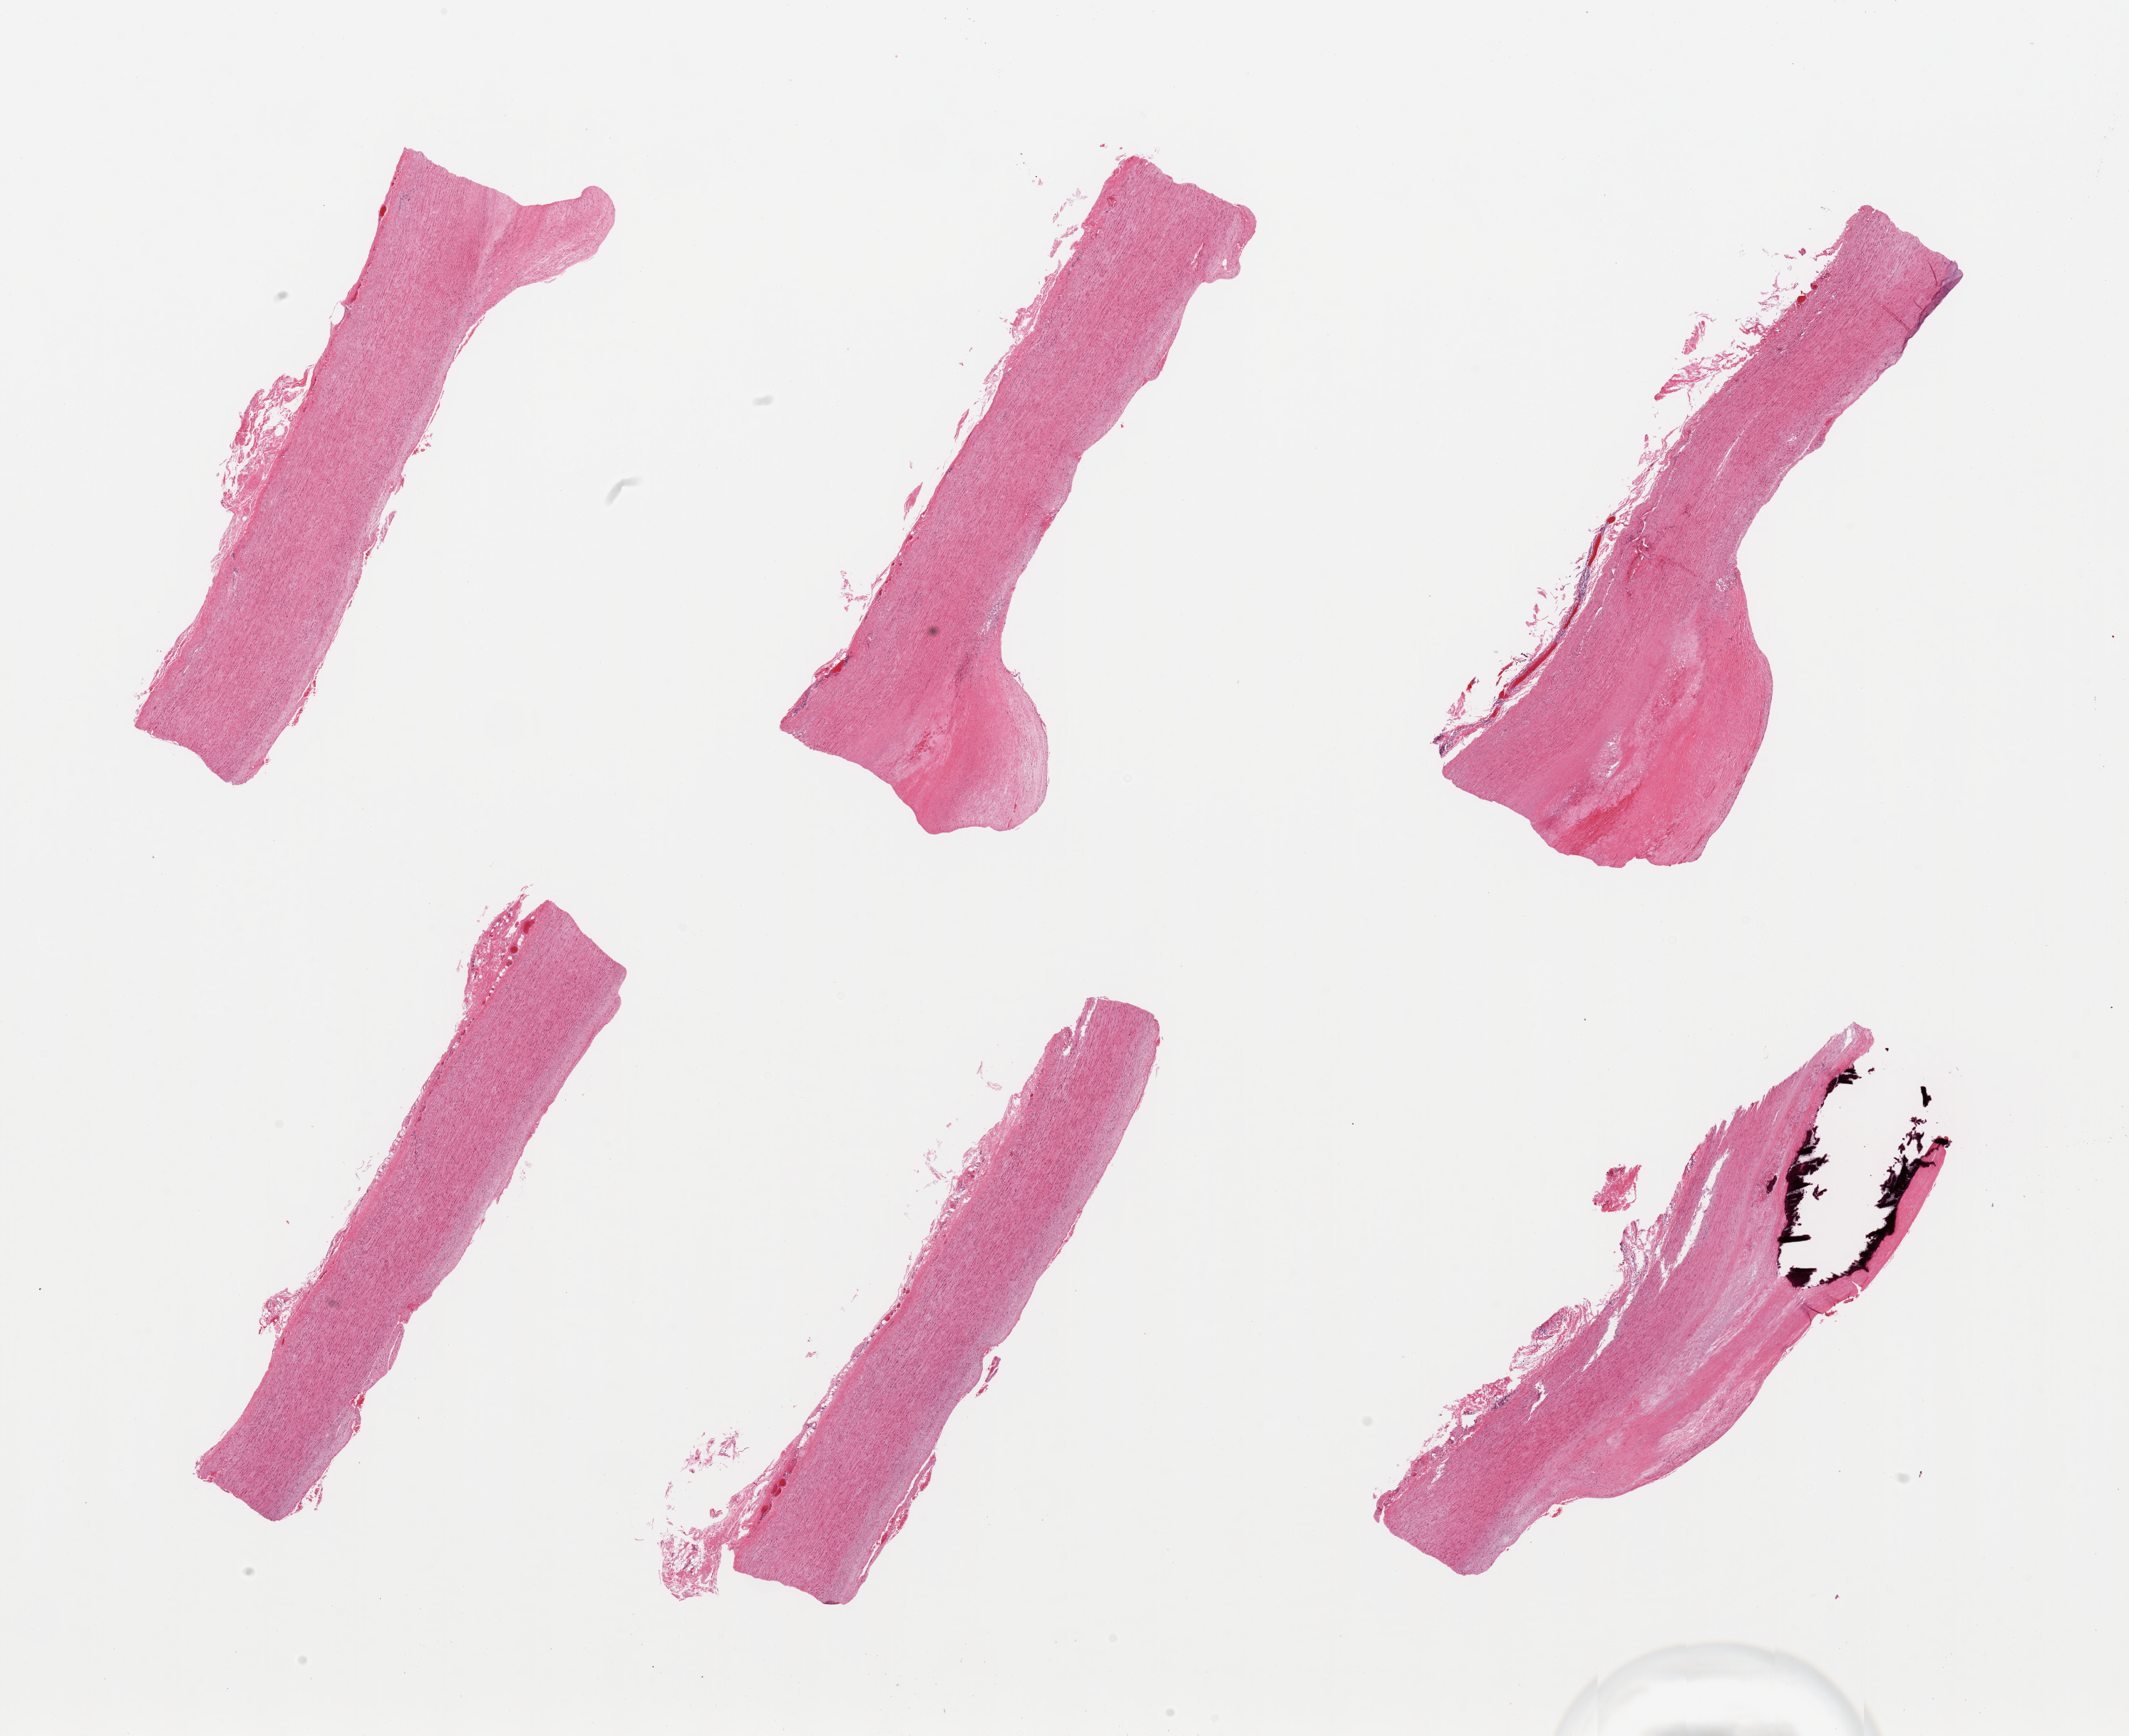
Whole-slide image, haematoxylin and eosin stain, low-resolution overview of the scanned area, about 23.6 x 19.3 mm (from a 20x scan), PAXgene-fixed, paraffin-embedded tissue, target tissue: aorta, donor tissue sample. Donor sex: male.
Pathologist's review note for this sample: 6 pieces; severe focal plaques with a large calcific deposit in 1 piece.